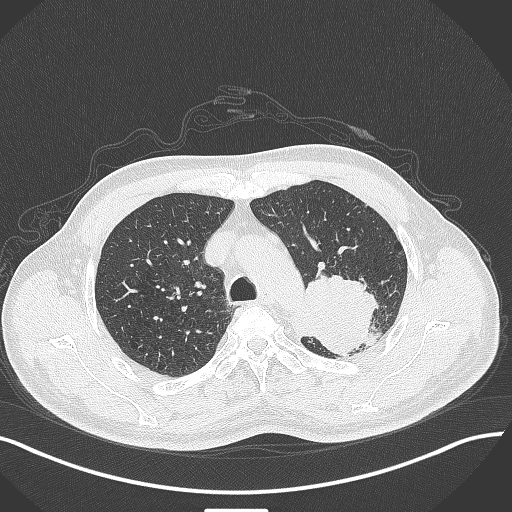
Chest CT, one axial slice. Position 319 of 429 along the scan axis. 120 kVp. Lung window (W 1500 / L -600 HU). 512 × 512 image matrix, field of view 400 × 400 mm. Patient: male, 55 years. Case-level facts recorded for this patient, not image findings: clinical TNM (as recorded): T3 N0 M1c; histopathological grade: G3.
Structures marked on this image (bounding box drawn by a radiologist):
- lung tumour (recorded histology: adenocarcinoma): bounding box [x1, y1, x2, y2] px = [290, 272, 382, 358]